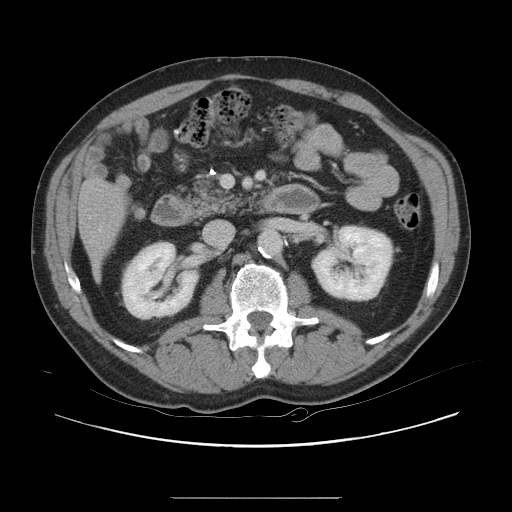
Contrast-enhanced abdominal CT, one axial slice; position 6 of 40 along the scan axis; 120 kVp; soft-tissue window (W 400 / L 40 HU); 5 mm slice thickness; 512 × 512 image matrix. Male patient, age 64 years. From the clinical record (not read from this slice): diagnosis: colorectal cancer liver metastases, imaged before liver resection; multiple liver metastases: yes; largest metastasis: 3.2 cm.
Structures marked on this image (manually delineated by an expert):
- hepatic veins: box from (x=100, y=228) to (x=102, y=230) px
- liver: (x=80, y=184)–(x=123, y=262)